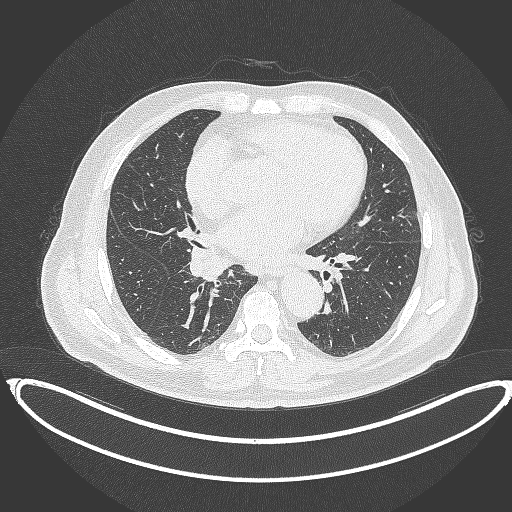
Chest CT, one axial slice; position 194 of 387 along the scan axis; reconstruction kernel B70f; 120 kVp; lung window (W 1500 / L -600 HU); 1 mm slice thickness; 512 × 512 image matrix. Patient: male, 61 years. From the clinical record (not read from this slice): clinical TNM (as recorded): T1b N1 M0.
Annotated regions visible in this slice (rectangle marked by the reading radiologist):
- lung tumour (recorded histology: squamous cell carcinoma): bounding box <188,246,238,282> (left, top, right, bottom; pixels)